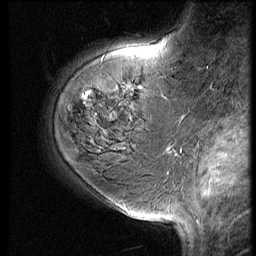
Breast MRI (dynamic contrast-enhanced), one sagittal slice; slice 19 of 60 in the series (ordered by position); 3 images stored at this slice position (order not interpretable as contrast timing); 1.5 T; TE 4.2 ms, TR 9 ms; 2.5 mm slice thickness; 256 × 256 image matrix. Female patient, age 59 years. From the clinical record (not read from this slice): setting: breast cancer imaged before/during neoadjuvant chemotherapy; receptor status: HER2-positive.
Structures marked on this image (semi-automatically segmented with operator editing):
- analysis volume of interest (the breast-tissue region the enhancement analysis was run in; not a lesion): bounding box (x1, y1, x2, y2) in pixels: (78, 61, 161, 125)
- tumour enhancement mask (voxels above the 140 % enhancement threshold inside the analysis volume of interest): (85, 92, 91, 99)